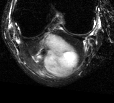
MRI of an extremity soft-tissue mass, one axial slice. Slice 14 of 44 in the series (ordered by position). T2-weighted fat-saturated. MR volume resampled by the dataset authors to the PET/CT grid (not the native acquisition matrix). 3.27 mm slice thickness. 114 × 103 image matrix. Female patient. From the clinical record (not read from this slice): histological type: liposarcoma; site of the primary tumour: right thigh.
Annotated regions visible in this slice (expert contour drawn on MRI and transferred to this co-registered scan by the dataset authors):
- gross tumour volume (mass): bounding box <31,32,80,78> (left, top, right, bottom; pixels)